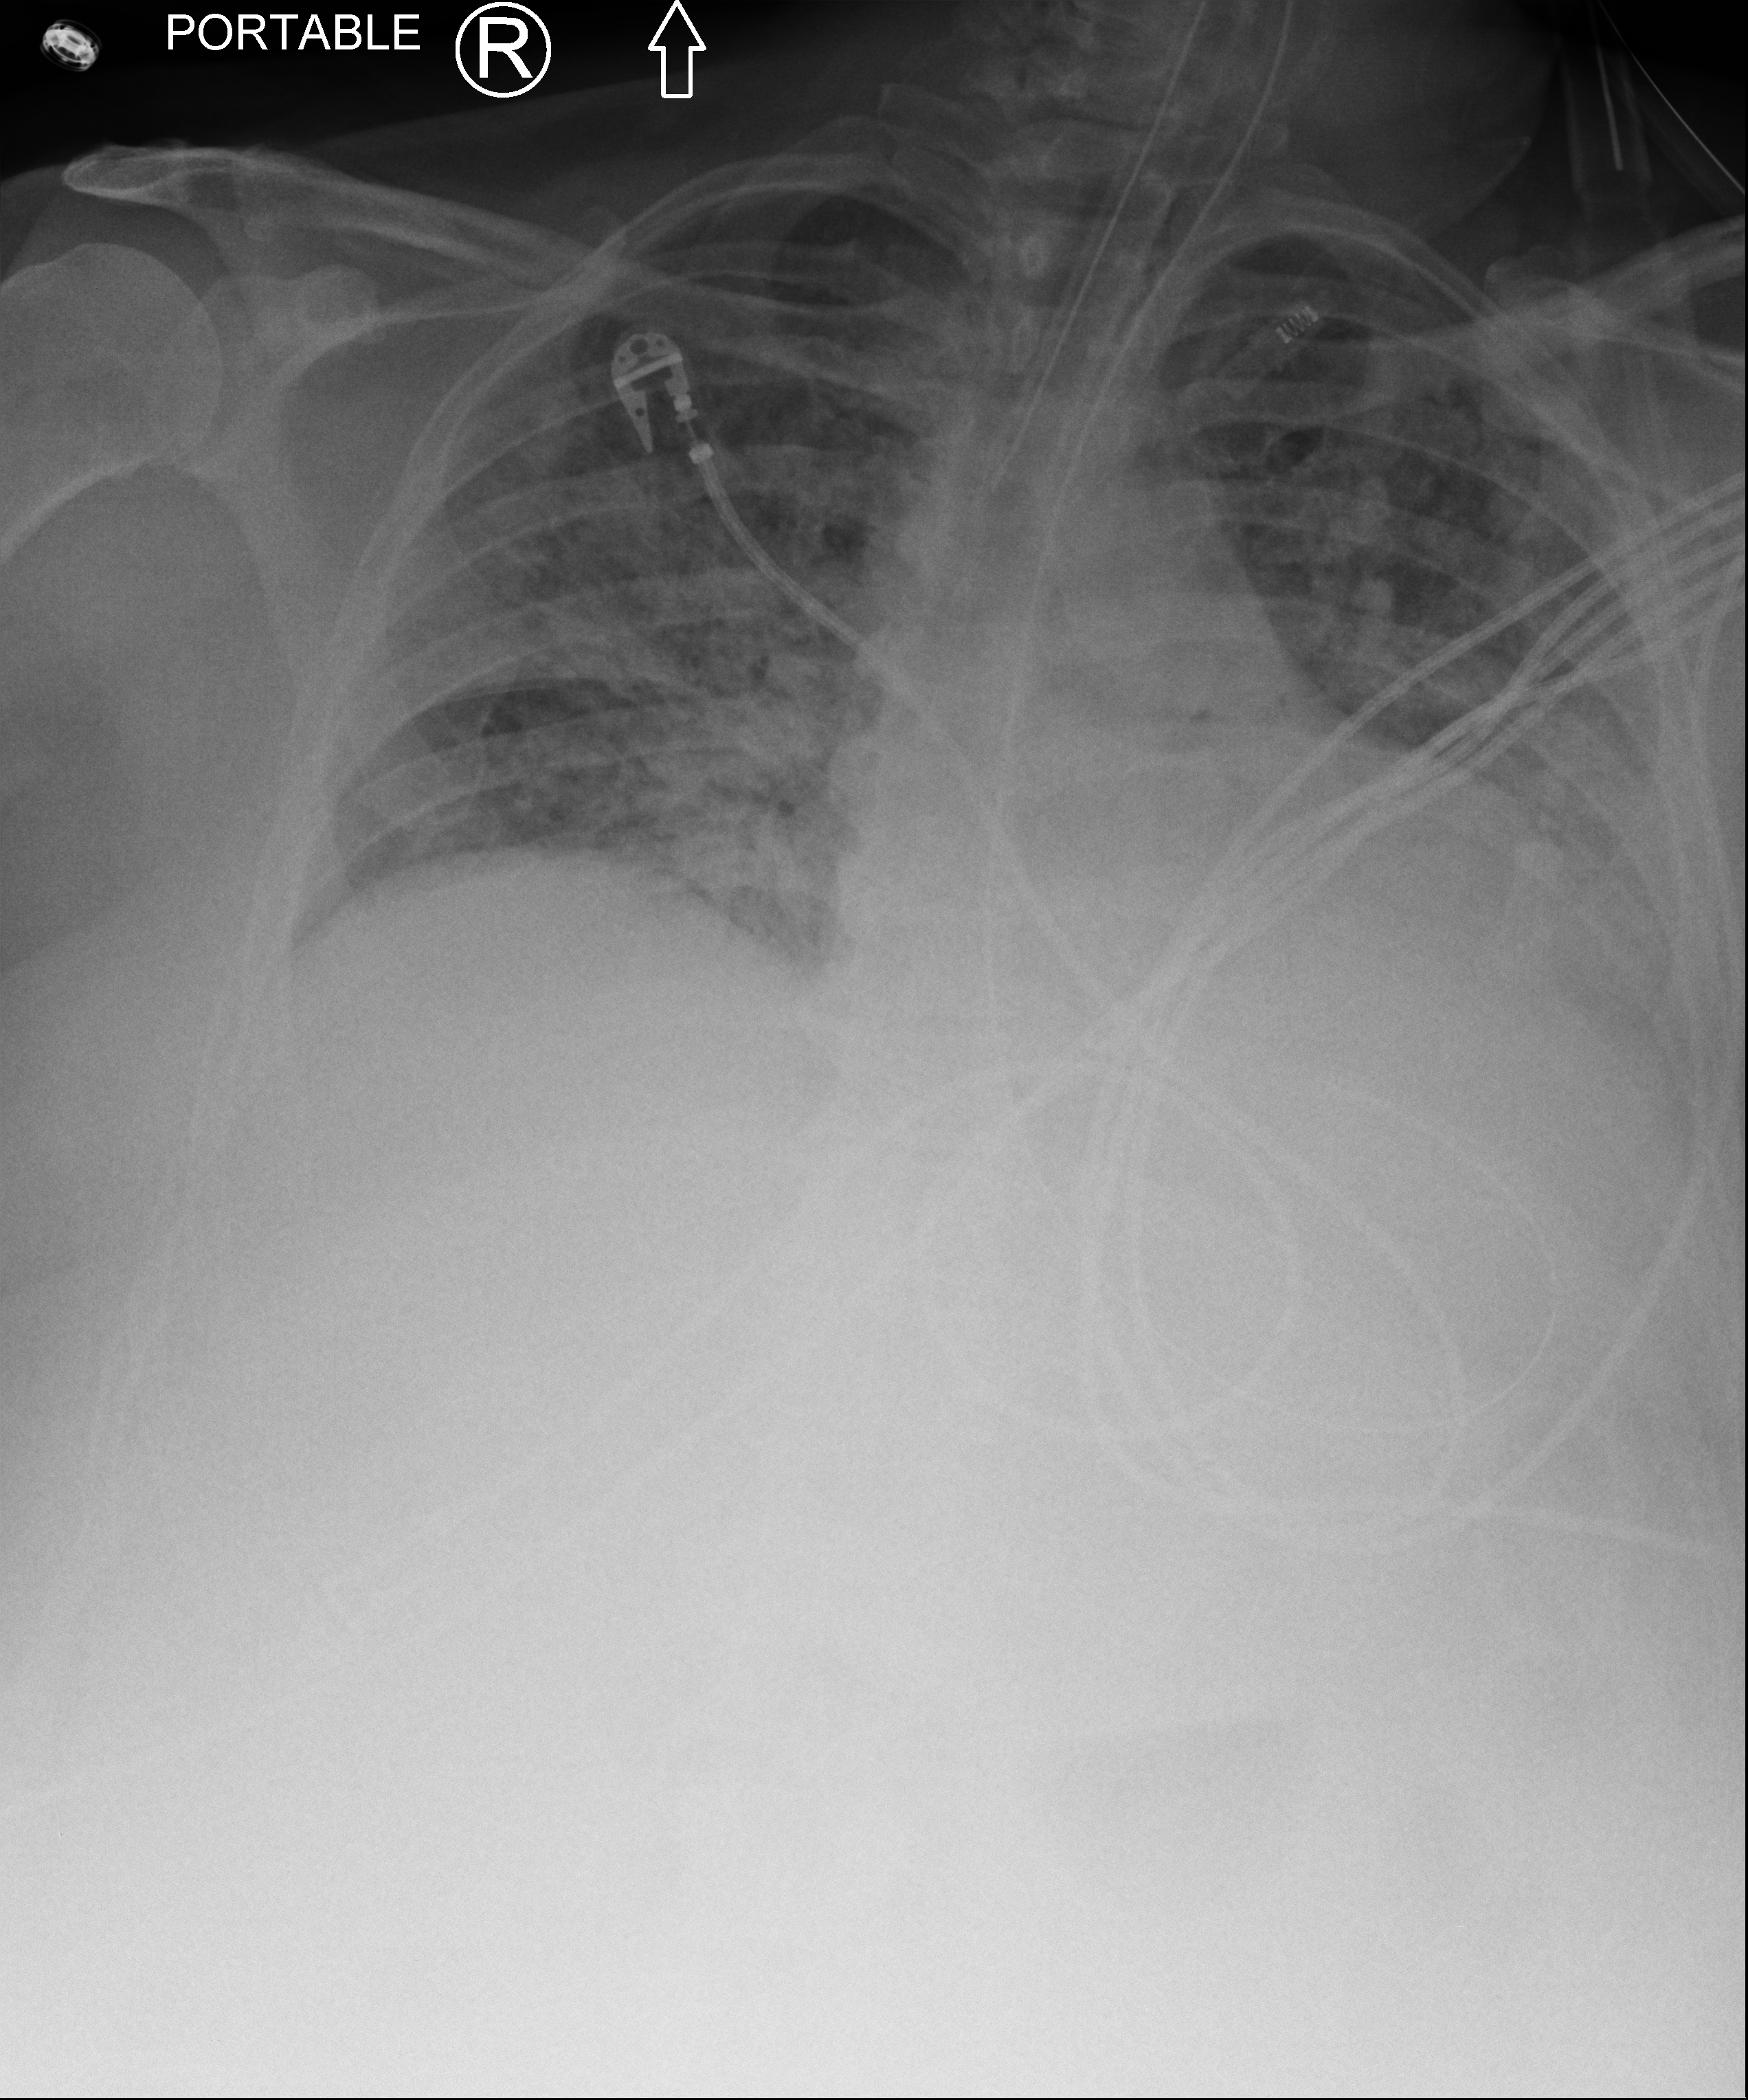
Bedside chest radiograph (computed radiography), anteroposterior (AP) projection. Adult patient hospitalised with COVID-19, age 18–59 years.
Hospital-stay facts (about this admission, not read from this image; timing relative to this image not recorded): admitted to intensive care during this hospital stay: yes; length of hospital stay: 28 days.